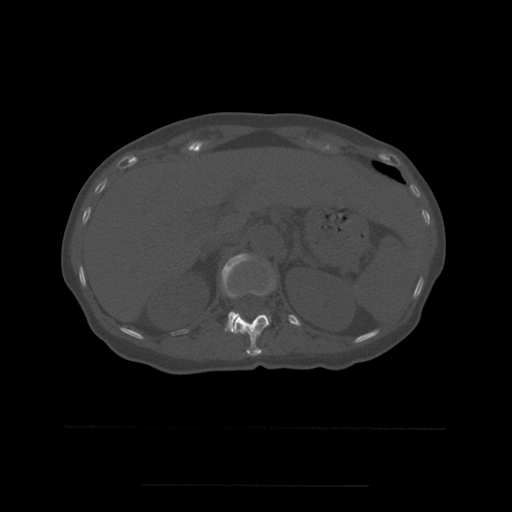
CT including the spine, one axial slice. Slice 249 of 544 in the series (ordered by position). Bone window (W 1800 / L 400 HU). 1.25 mm slice thickness. 512 × 512 image matrix, field of view 350 × 350 mm. Patient age 58 years. Case-level facts recorded for this patient, not image findings: primary cancer: lung.
Annotated regions visible in this slice (semi-automatically segmented with operator editing):
- L1 vertebra: box from (x=222, y=254) to (x=271, y=333) px
- T12 vertebra: (x=233, y=276)–(x=276, y=356)